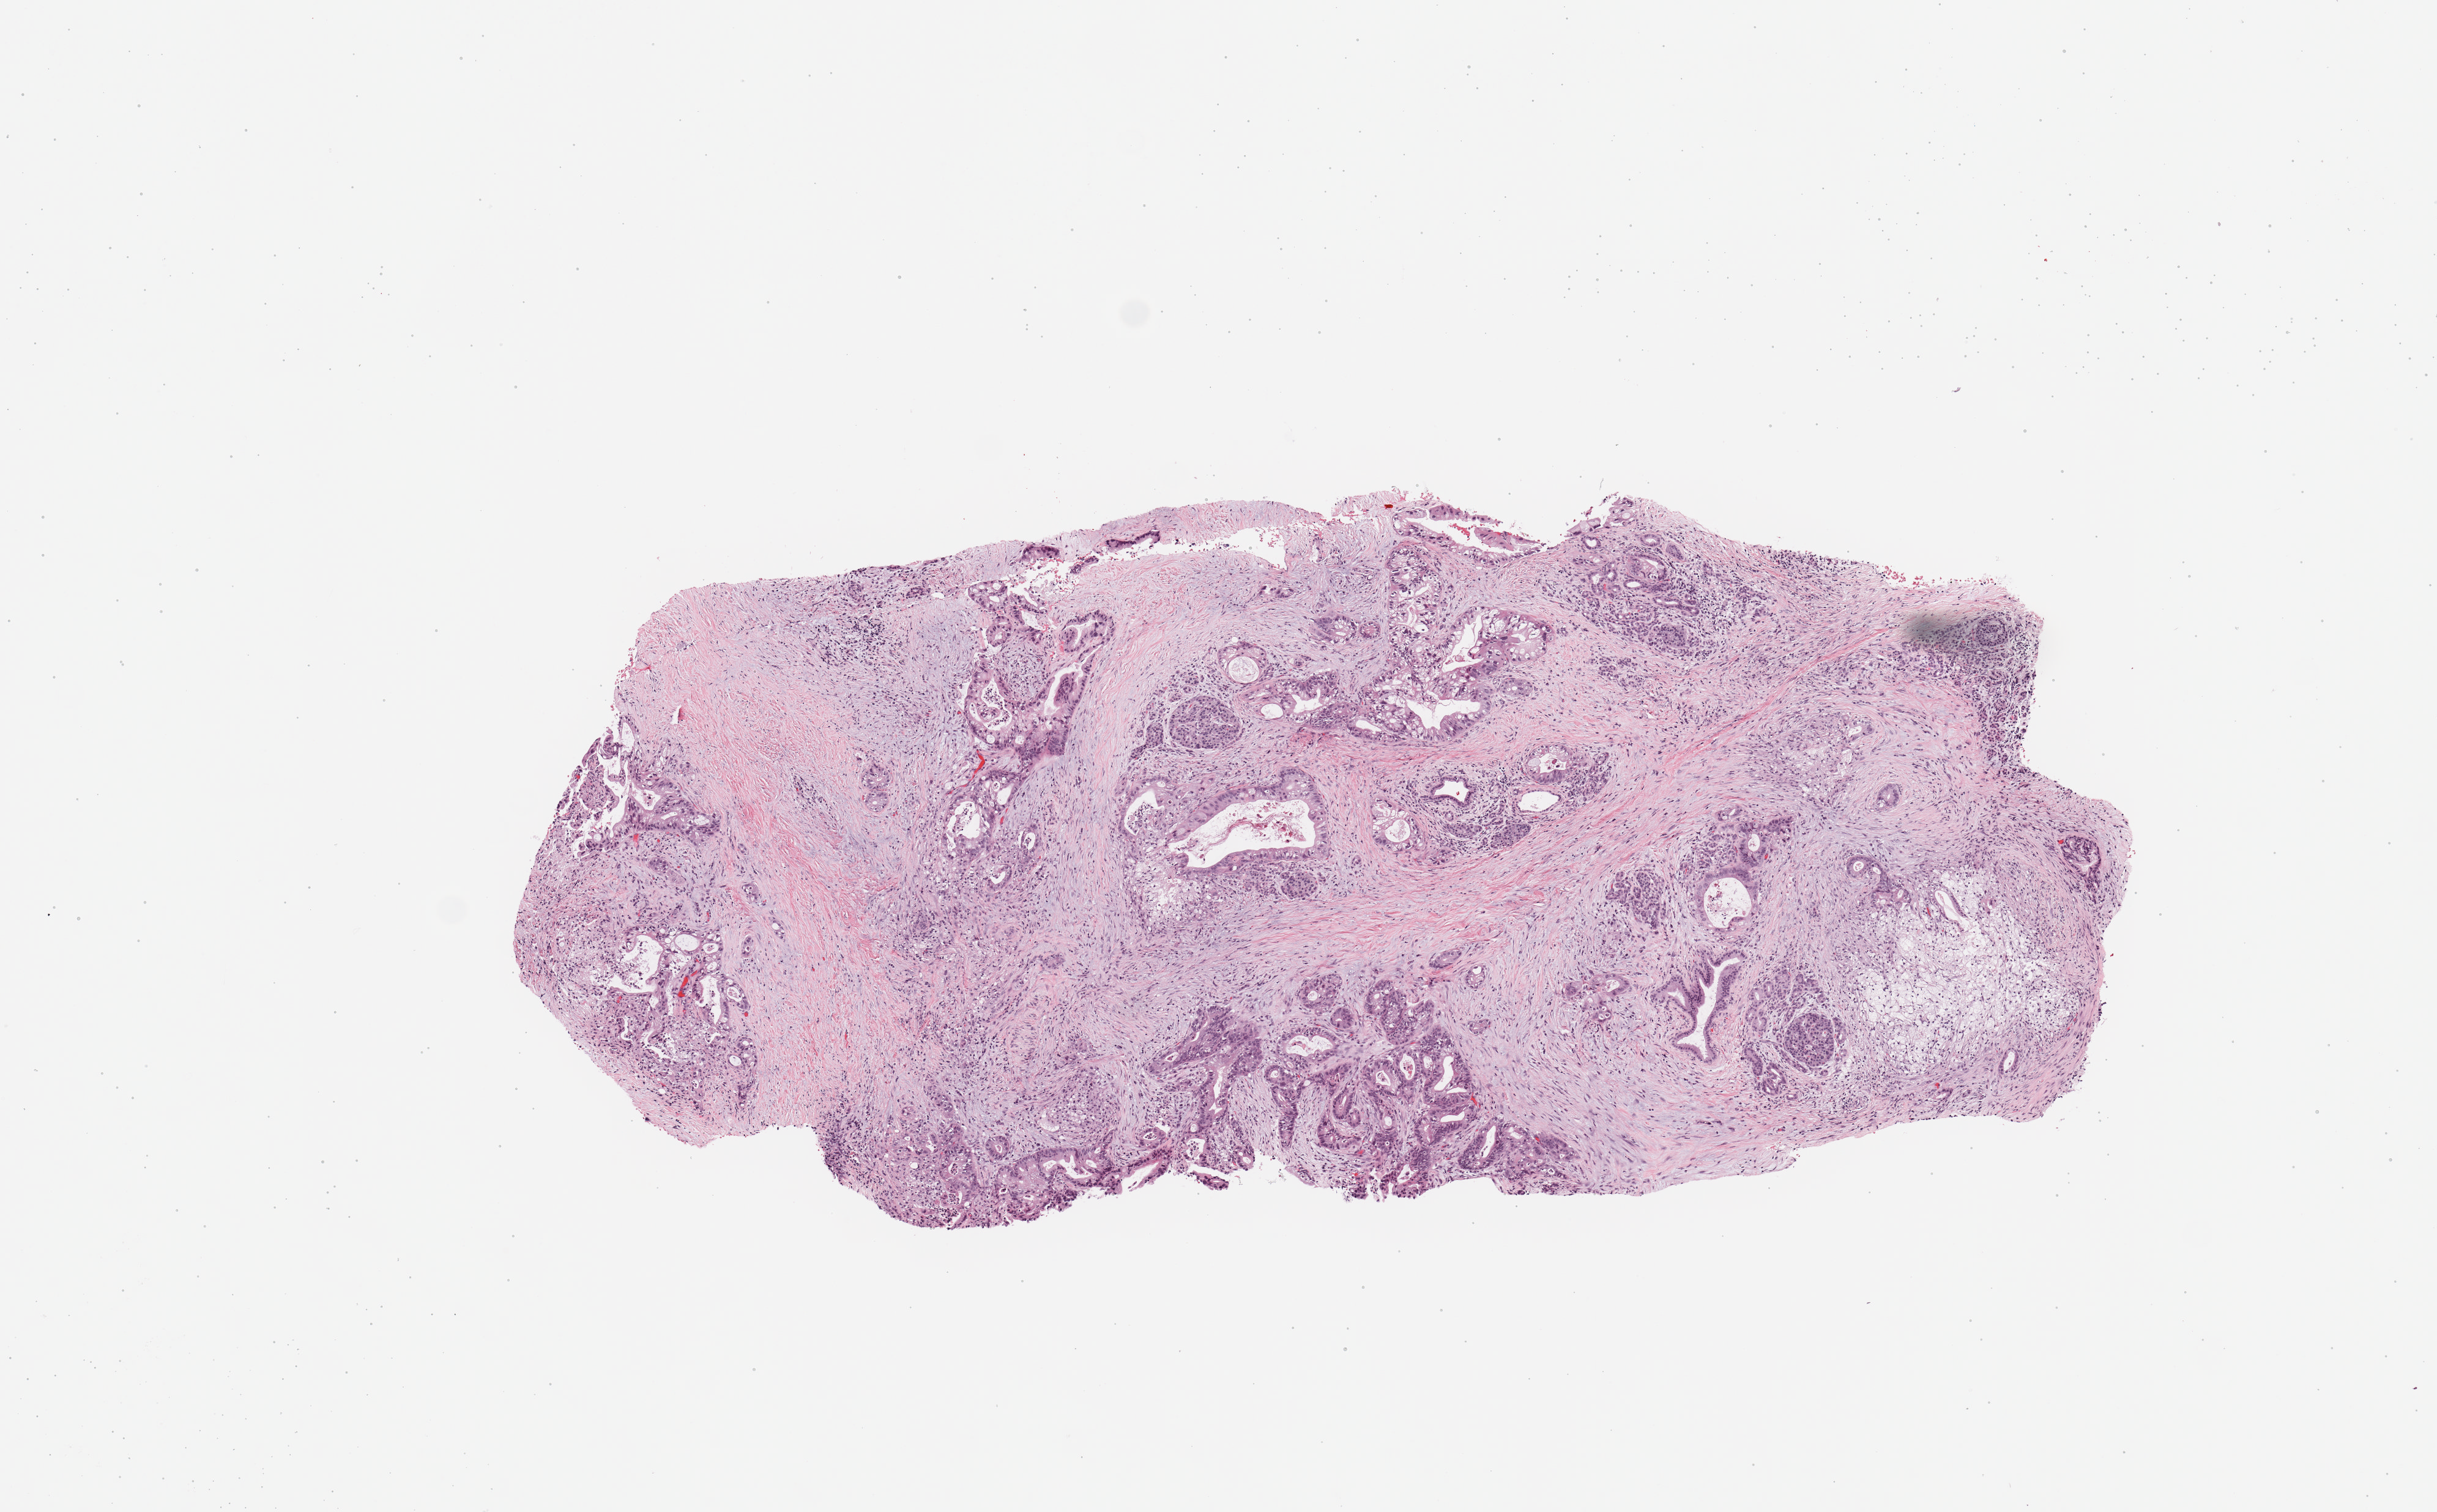
Whole-slide histology image, H&E-stained — whole scanned area (about 7.9 x 4.9 mm) shown as a low-resolution overview. Tumour tissue sample, sampled site: pancreas. Patient: female, age 78 years. Histologic grade: G2 (moderately differentiated). Slide review estimates, as recorded: tumour nuclei 40%, necrosis 10%.
• primary tumour site (as recorded): body
• AJCC pathologic stage: IIB
• diagnosis: Infiltrating duct carcinoma, NOS